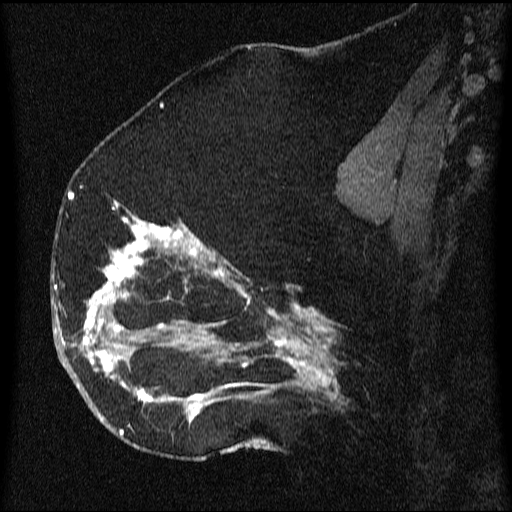
Breast MRI (dynamic contrast-enhanced), one sagittal slice. Slice 33 of 64 in the series (ordered by position). Dynamic contrast-enhanced series, image 2 of 3 at this slice position (ordered by acquisition). 1.5 T. TE 4.2 ms, TR 9.1 ms. 512 × 512 image matrix, field of view 180 × 180 mm. Patient: female, 52 years.
Annotated regions visible in this slice (semi-automatic segmentation, software-assisted and operator-edited):
- analysis volume of interest (the breast-tissue region the enhancement analysis was run in; not a lesion): bounding box <61,203,350,438> (left, top, right, bottom; pixels)
- tumour enhancement mask (voxels above the 70 % enhancement threshold inside the analysis volume of interest): <61,203,339,437>